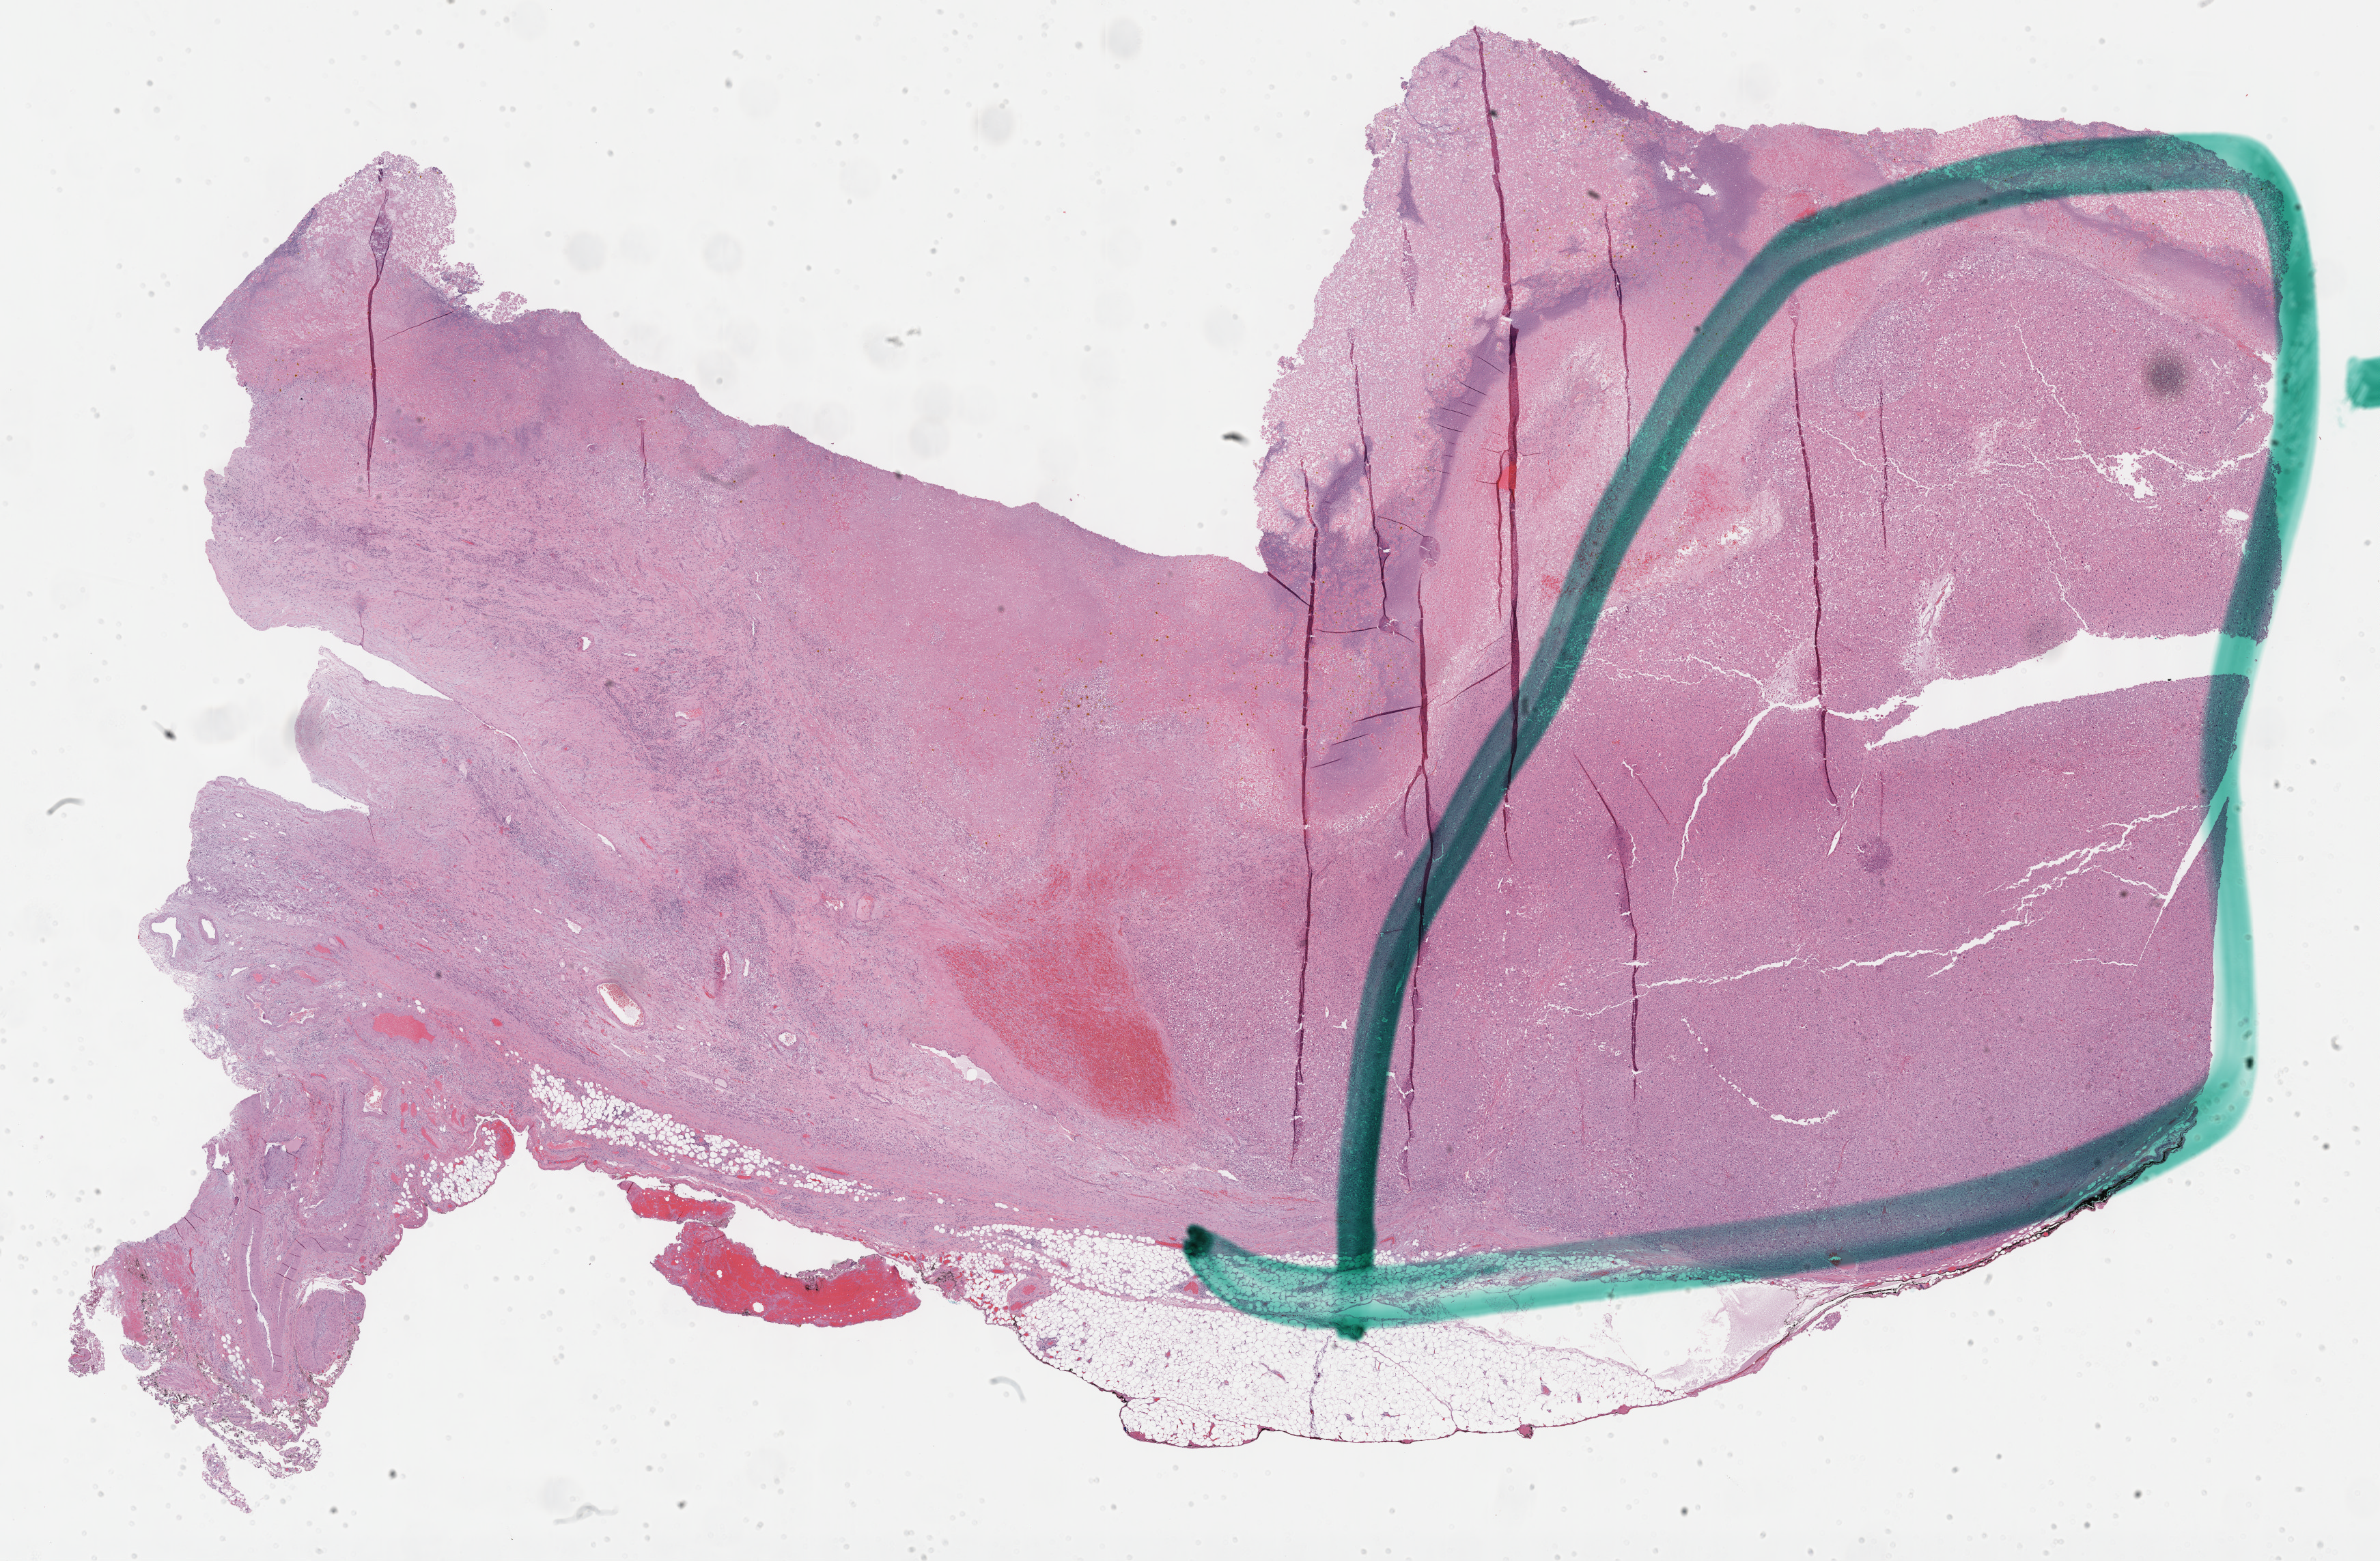
Whole-slide histology image, H&E-stained — whole scanned area (about 28.2 x 18.5 mm, acquisition: 40x scan) shown as a low-resolution overview. Formalin-fixed paraffin-embedded (FFPE) diagnostic section. Sample: primary tumour, adrenal cortex. Female, age 65 years at initial diagnosis.
Lymph nodes positive (case pathology): 0 of 17 examined. Histologic diagnosis: Adrenal cortical carcinoma (cortex of adrenal gland). Laterality: left.